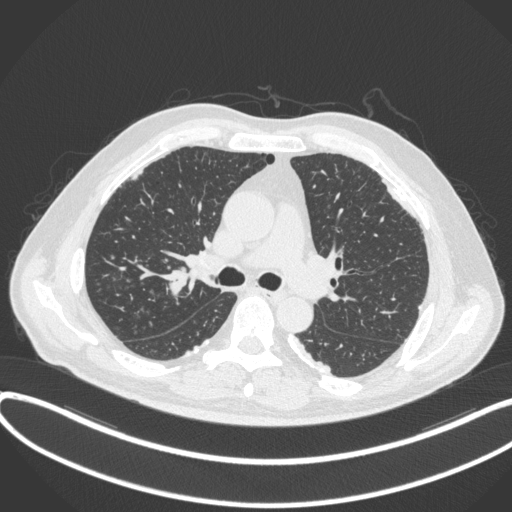
Chest CT, one axial slice; position 263 of 455 along the scan axis; reconstruction kernel B31f; 120 kVp; lung window (W 1500 / L -600 HU); 1 mm slice thickness; 512 × 512 image matrix, field of view 400 × 400 mm. Male patient, age 58 years. From the clinical record (not read from this slice): clinical TNM (as recorded): T1c N0 M0.
Annotated regions visible in this slice (rectangle marked by the reading radiologist):
- lung tumour (recorded histology: squamous cell carcinoma): bounding box (x1, y1, x2, y2) in pixels: (162, 260, 193, 300)